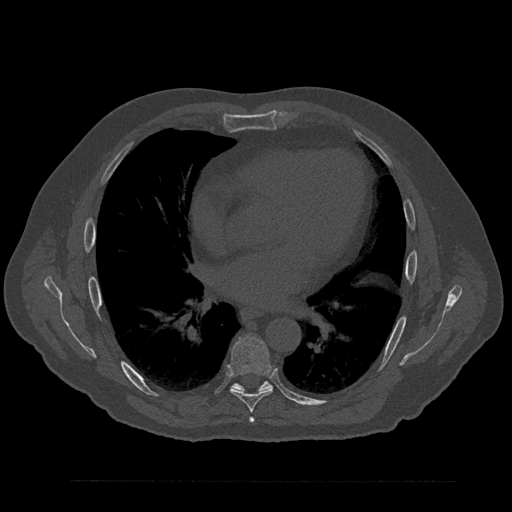
CT including the spine, one axial slice. Position 491 of 797 along the scan axis. Reconstruction kernel Br40s/3. Bone window (W 1800 / L 400 HU). 0.5 mm slice thickness. 512 × 512 image matrix, field of view 430 × 430 mm. Male patient, age 61 years. Case-level facts recorded for this patient, not image findings: primary cancer: prostate.
Structures marked on this image (semi-automatically segmented with operator editing):
- T6 vertebra: bounding box (x1, y1, x2, y2) in pixels: (249, 418, 254, 423)
- T7 vertebra: (228, 335, 273, 413)
- T8 vertebra: (232, 381, 272, 392)